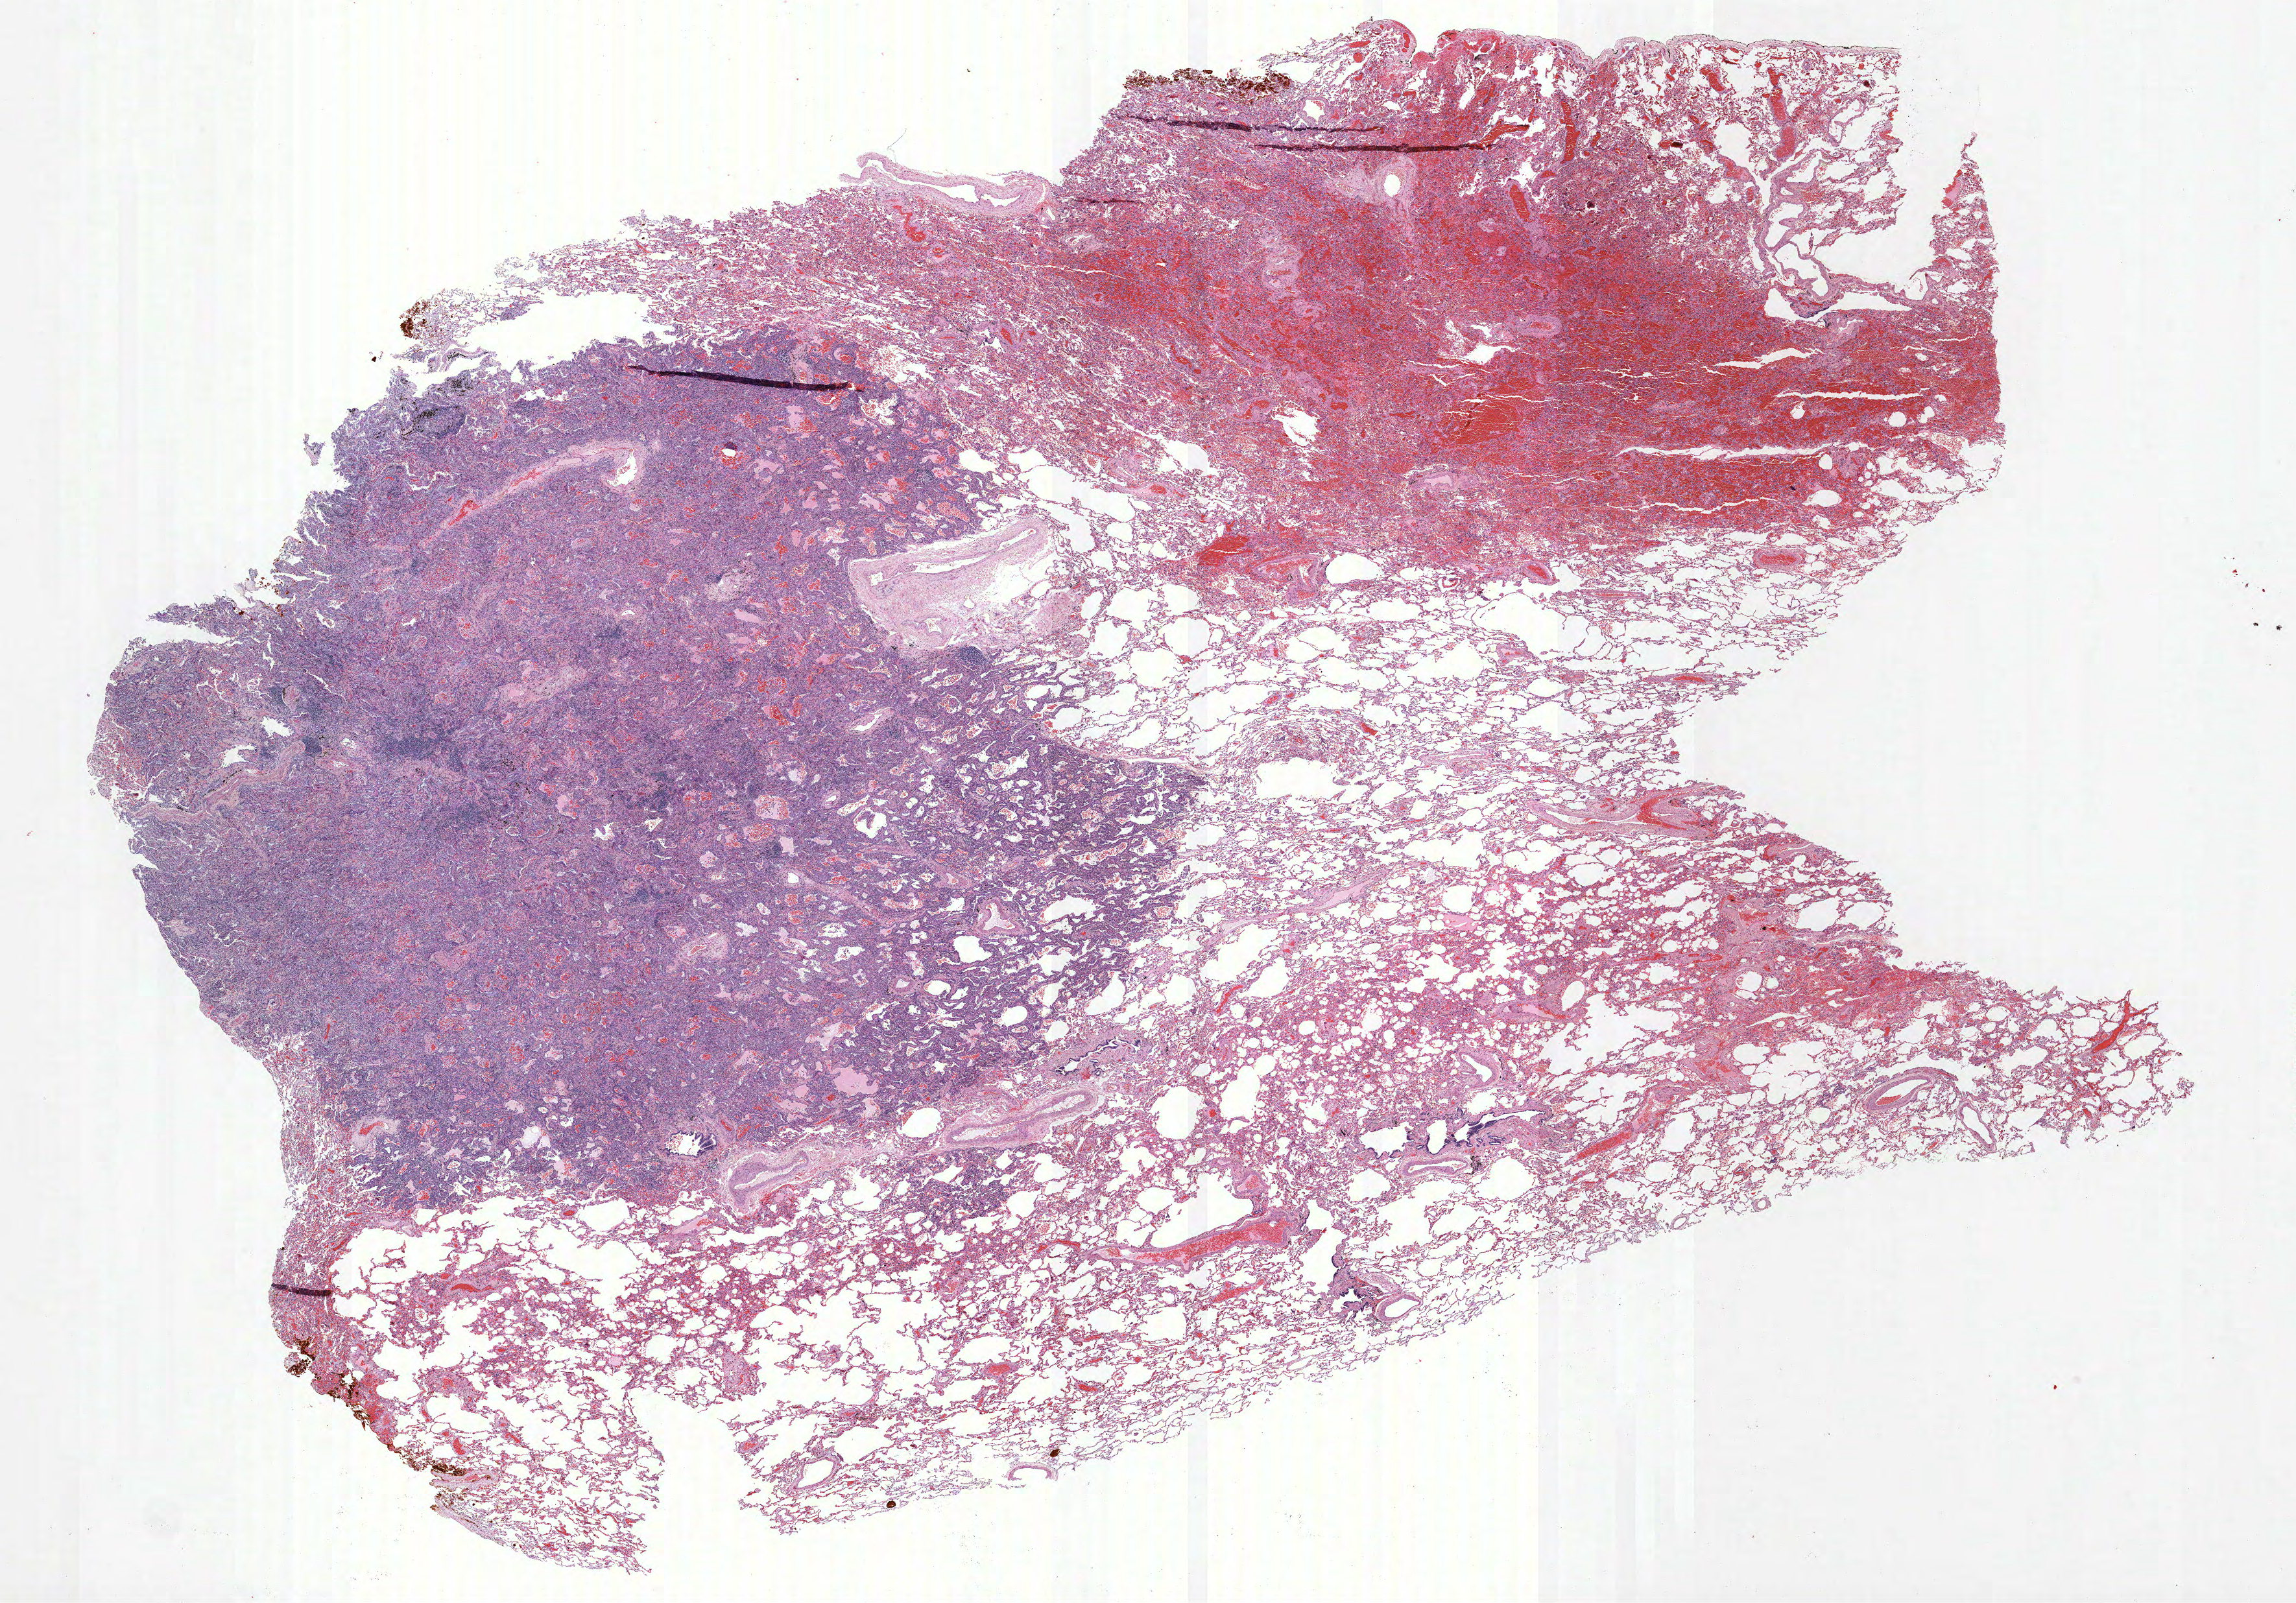
Whole-slide histology image, Hematoxylin and eosin (H&E) stained, a low-resolution overview of the entire scanned area, about 28.3 x 19.8 mm; formalin-fixed paraffin-embedded (FFPE) section; lung tissue. Male, age 62 at enrolment. Former smoker at enrolment. Grade: well differentiated (G1).
Tumour size (pathology): 14 mm. Stage (AJCC 6th edition): IA. Primary tumour location (clinical record): right lower lobe. Participant's lung-cancer diagnosis: Bronchiolo-alveolar carcinoma, non-mucinous (ICD-O-3 8252/3).